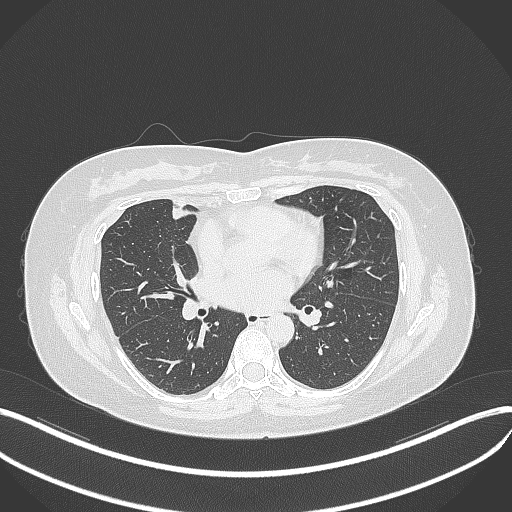
Chest CT, one axial slice; position 154 of 273 along the scan axis; reconstruction kernel B70f; 120 kVp; lung window (W 1500 / L -600 HU); 1 mm slice thickness; 512 × 512 image matrix, field of view 400 × 400 mm. Patient: female, 42 years. From the clinical record (not read from this slice): clinical TNM (as recorded): T1b N0 M0.
Structures marked on this image (rectangle marked by the reading radiologist):
- lung tumour (recorded histology: adenocarcinoma): bounding box (x1, y1, x2, y2) in pixels: (163, 200, 200, 228)